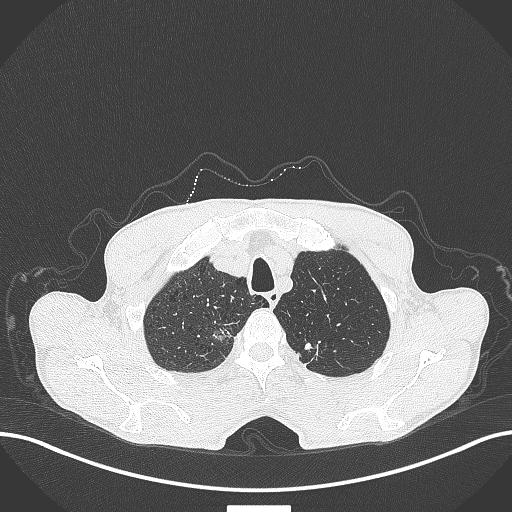
Chest CT, one axial slice; position 374 of 445 along the scan axis; reconstruction kernel B70f; lung window (W 1500 / L -600 HU); 1 mm slice thickness; 512 × 512 image matrix, field of view 400 × 400 mm. Patient: male, 70 years. From the clinical record (not read from this slice): clinical TNM (as recorded): T1a N0 M0; histopathological grade: G1-2.
Annotated regions visible in this slice (rectangle marked by the reading radiologist):
- lung tumour (recorded histology: adenocarcinoma): box from (x=209, y=322) to (x=237, y=346) px